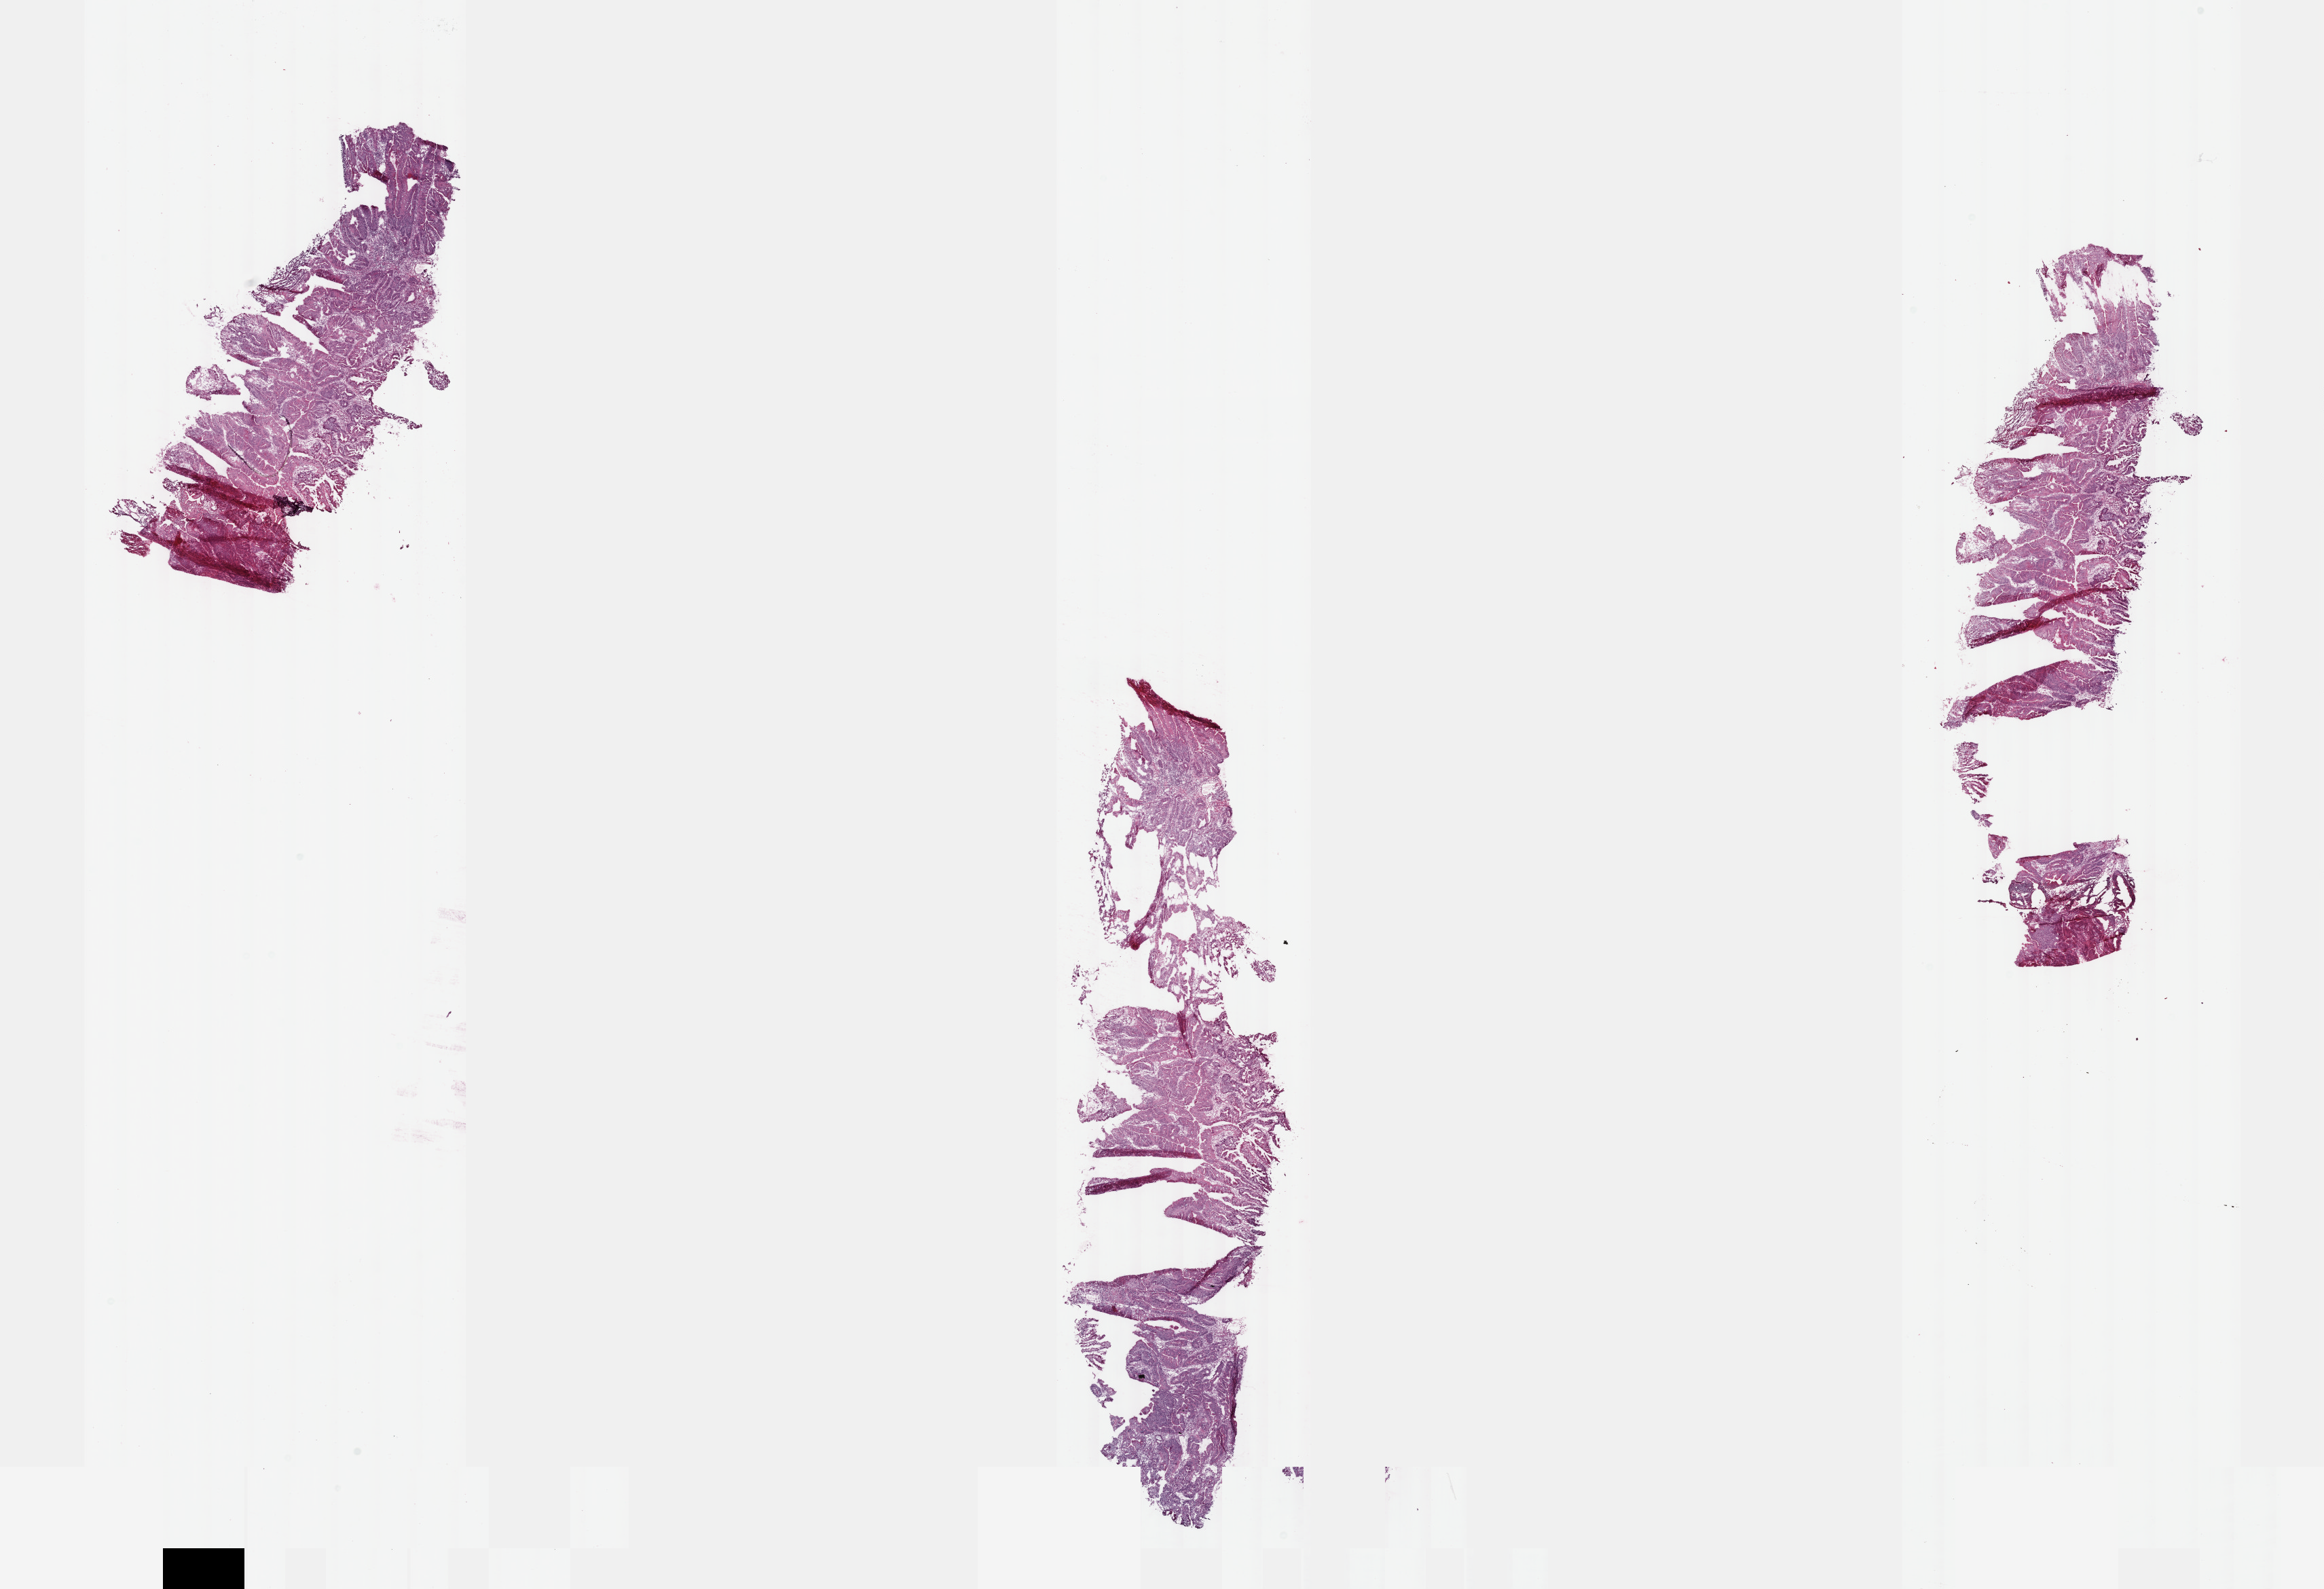
Hematoxylin and eosin (H&E) stained whole-slide image, low-resolution overview of the scanned area, about 27.7 x 18.9 mm (acquisition: 40x scan). Frozen section. Sample: primary tumour, colon. Male, age 67 years at initial diagnosis. Pathologist review of this section (percent, as recorded): tumour cells 88%, tumour nuclei 85%, normal cells 0%, stromal cells 10%, necrosis 2%. Inflammatory infiltration, as recorded: lymphocyte infiltration 8%, monocyte infiltration 1%, neutrophil infiltration 2%.
• pathologic diagnosis: Adenocarcinoma, NOS (cecum)
• AJCC pathologic stage: II
• lymph nodes positive (case pathology): 0 of 27 examined